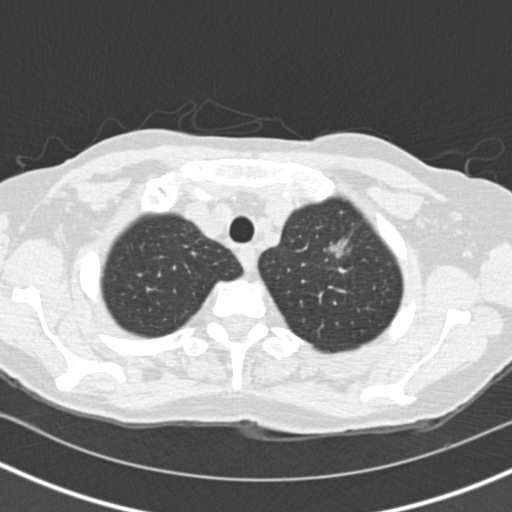
Axial slice from a low-dose chest CT screening exam. First (baseline) screen. Lung window (W 1500 / L -600 HU). Slice 22 of 146 in the series. 512 × 512 image matrix. Female, age 73 years at enrolment.
Expert-annotated lung lesion, bounding box <308,229,359,288> (left, top, right, bottom; pixels). The exam's reader record, not a measurement of the box and not confirmed to be the same lesion: non-calcified nodule or mass ≥4 mm, left upper lobe, 27 × 21 mm, spiculated (stellate) margins, soft tissue attenuation. Official screen result: positive, change unspecified: nodule(s) >= 4 mm or enlarging nodule(s), mass(es), or other non-specific abnormalities suspicious for lung cancer. Later outcome: lung cancer diagnosed 72 days after this screen — bronchiolo-alveolar adenocarcinoma, NOS, left upper lobe, moderately differentiated (G2), stage IIIB (AJCC 6th edition), 17 mm at pathology.